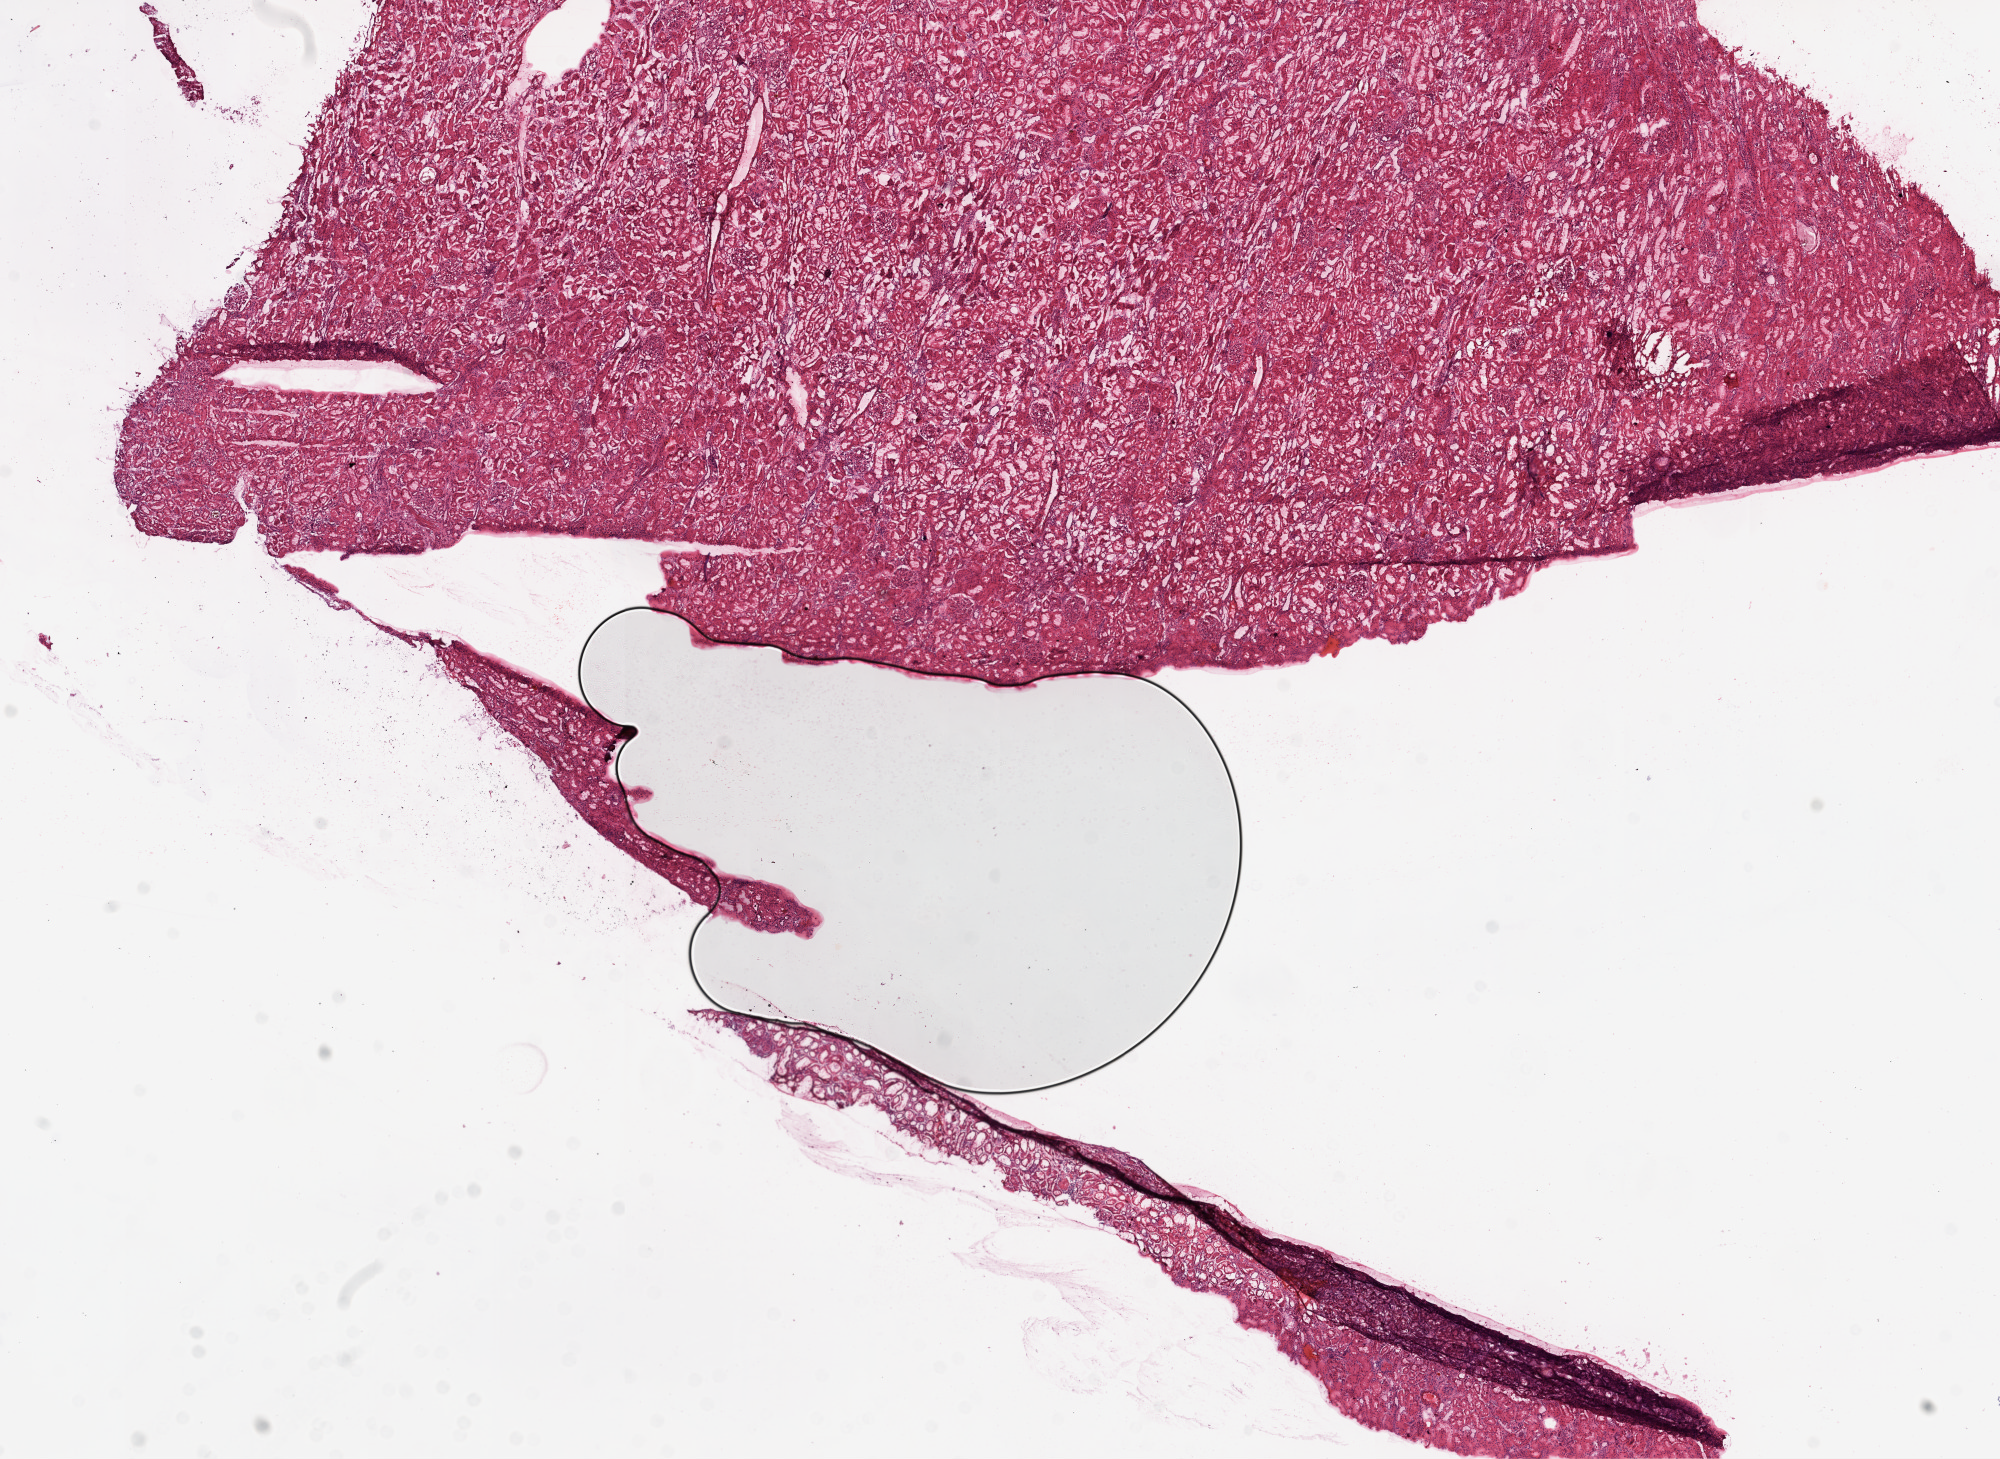
H&E whole-slide image, a low-resolution overview of the entire scanned area, about 16.0 x 11.7 mm; frozen section from the top of the tissue portion; solid tissue normal (non-tumour tissue) sample from the kidney. Female, age 78 years at initial diagnosis.
This section: solid tissue normal sample (biorepository sample class). Patient diagnosis: Clear cell adenocarcinoma, NOS.